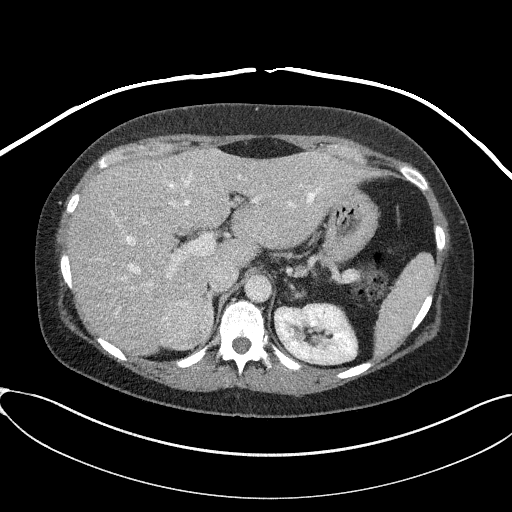
Contrast-enhanced abdominal CT, one axial slice; position 59 of 95 along the scan axis; reconstruction kernel I41f/2; soft-tissue window (W 400 / L 40 HU); 3 mm slice thickness; 512 × 512 image matrix. Patient: female, 46 years. Case-level facts recorded for this patient, not image findings: diagnosis: adrenocortical carcinoma; tumour side: right adrenal; tumour size at pathology: 7.2 cm; Ki-67 index: 50 %; stage (as recorded): 4.
Outlined on this slice (semi-automatically segmented with operator editing):
- mass: bounding box (x1, y1, x2, y2) in pixels: (158, 297, 213, 349)